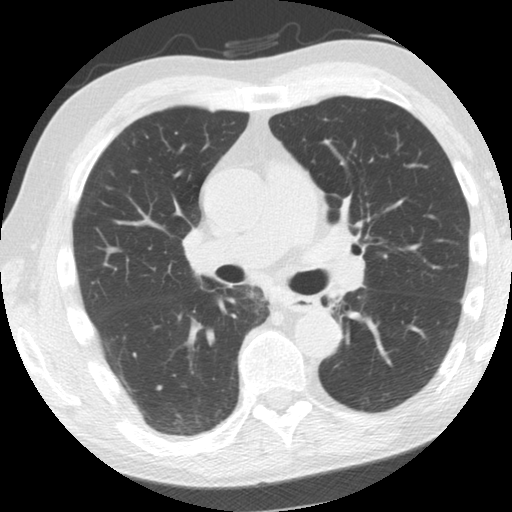
Chest CT (low-dose screening protocol), one axial image, second screening round (one year after baseline), lung window (W 1500 / L -600 HU). Male participant, aged 61 years at enrolment. Former smoker at enrolment.
- Lesion marked by an expert reader, box from (x=305, y=287) to (x=349, y=322) px.
- Screening reader's record for this exam: no non-calcified nodule ≥4 mm recorded.
- Official screen result: negative screen, minor abnormalities not suspicious for lung cancer.
- Later outcome: lung cancer diagnosed 775 days after this screen — squamous cell carcinoma, NOS, left upper lobe, left lower lobe, well differentiated (G1), stage IIB (AJCC 6th edition), 100 mm at pathology.